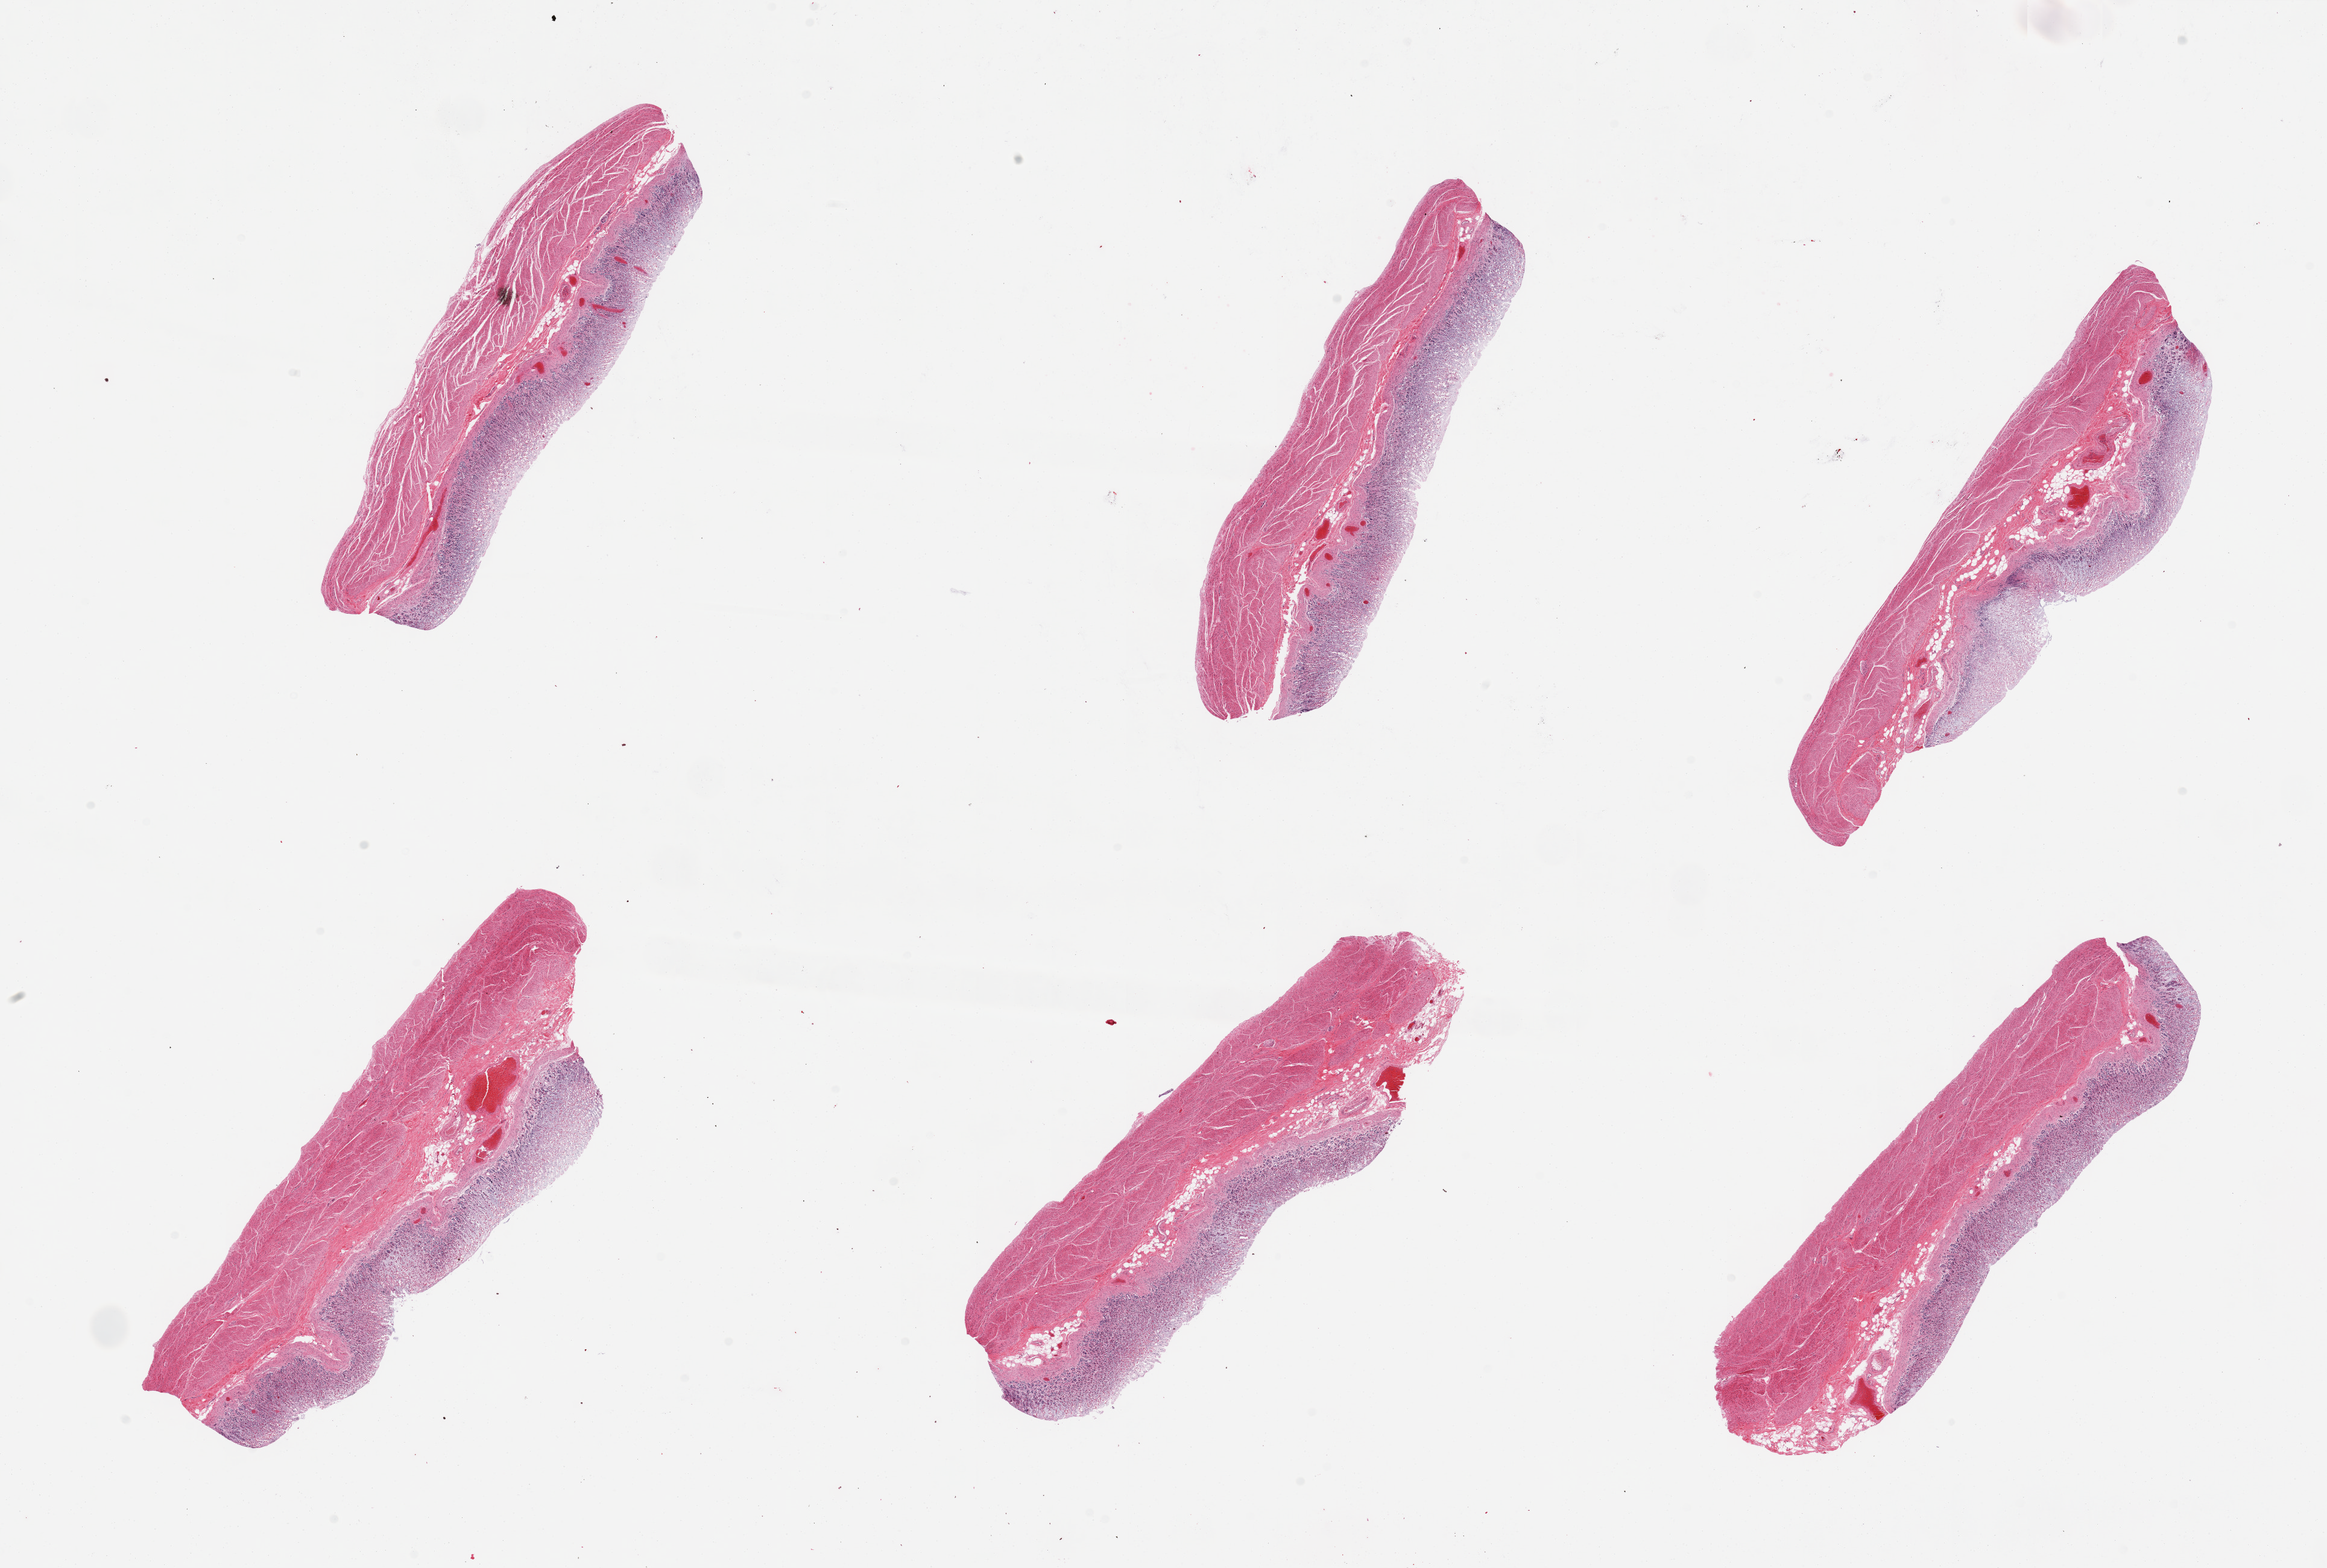
Whole-slide image, H&E stain, brightfield, shown as a low-resolution overview of the whole scanned area (about 30.5 x 20.6 mm), PAXgene-fixed, paraffin-embedded tissue, sampled site (target tissue): stomach, donor tissue sample. Donor sex: male.
- pathologist's review note for this sample: 6 pieces; mucosa=3, muscle=2